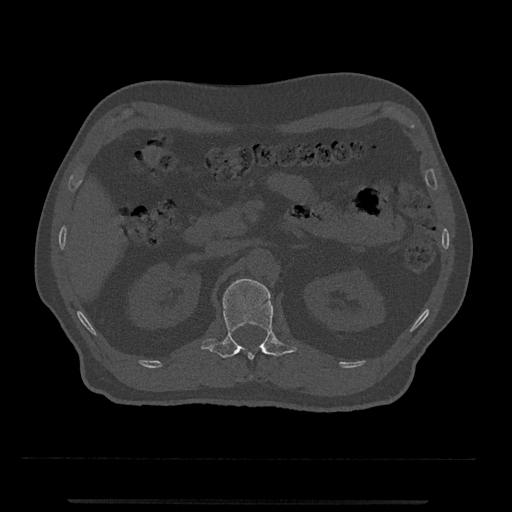
CT including the spine, one axial slice. Slice 342 of 797 in the series (ordered by position). Bone window (W 1800 / L 400 HU). 0.5 mm slice thickness. 512 × 512 image matrix, field of view 419 × 419 mm. Patient: male, 63 years. Case-level facts recorded for this patient, not image findings: primary cancer: prostate.
Annotated regions visible in this slice (semi-automatically segmented with operator editing):
- L1 vertebra: bounding box (x1, y1, x2, y2) in pixels: (201, 278, 297, 360)